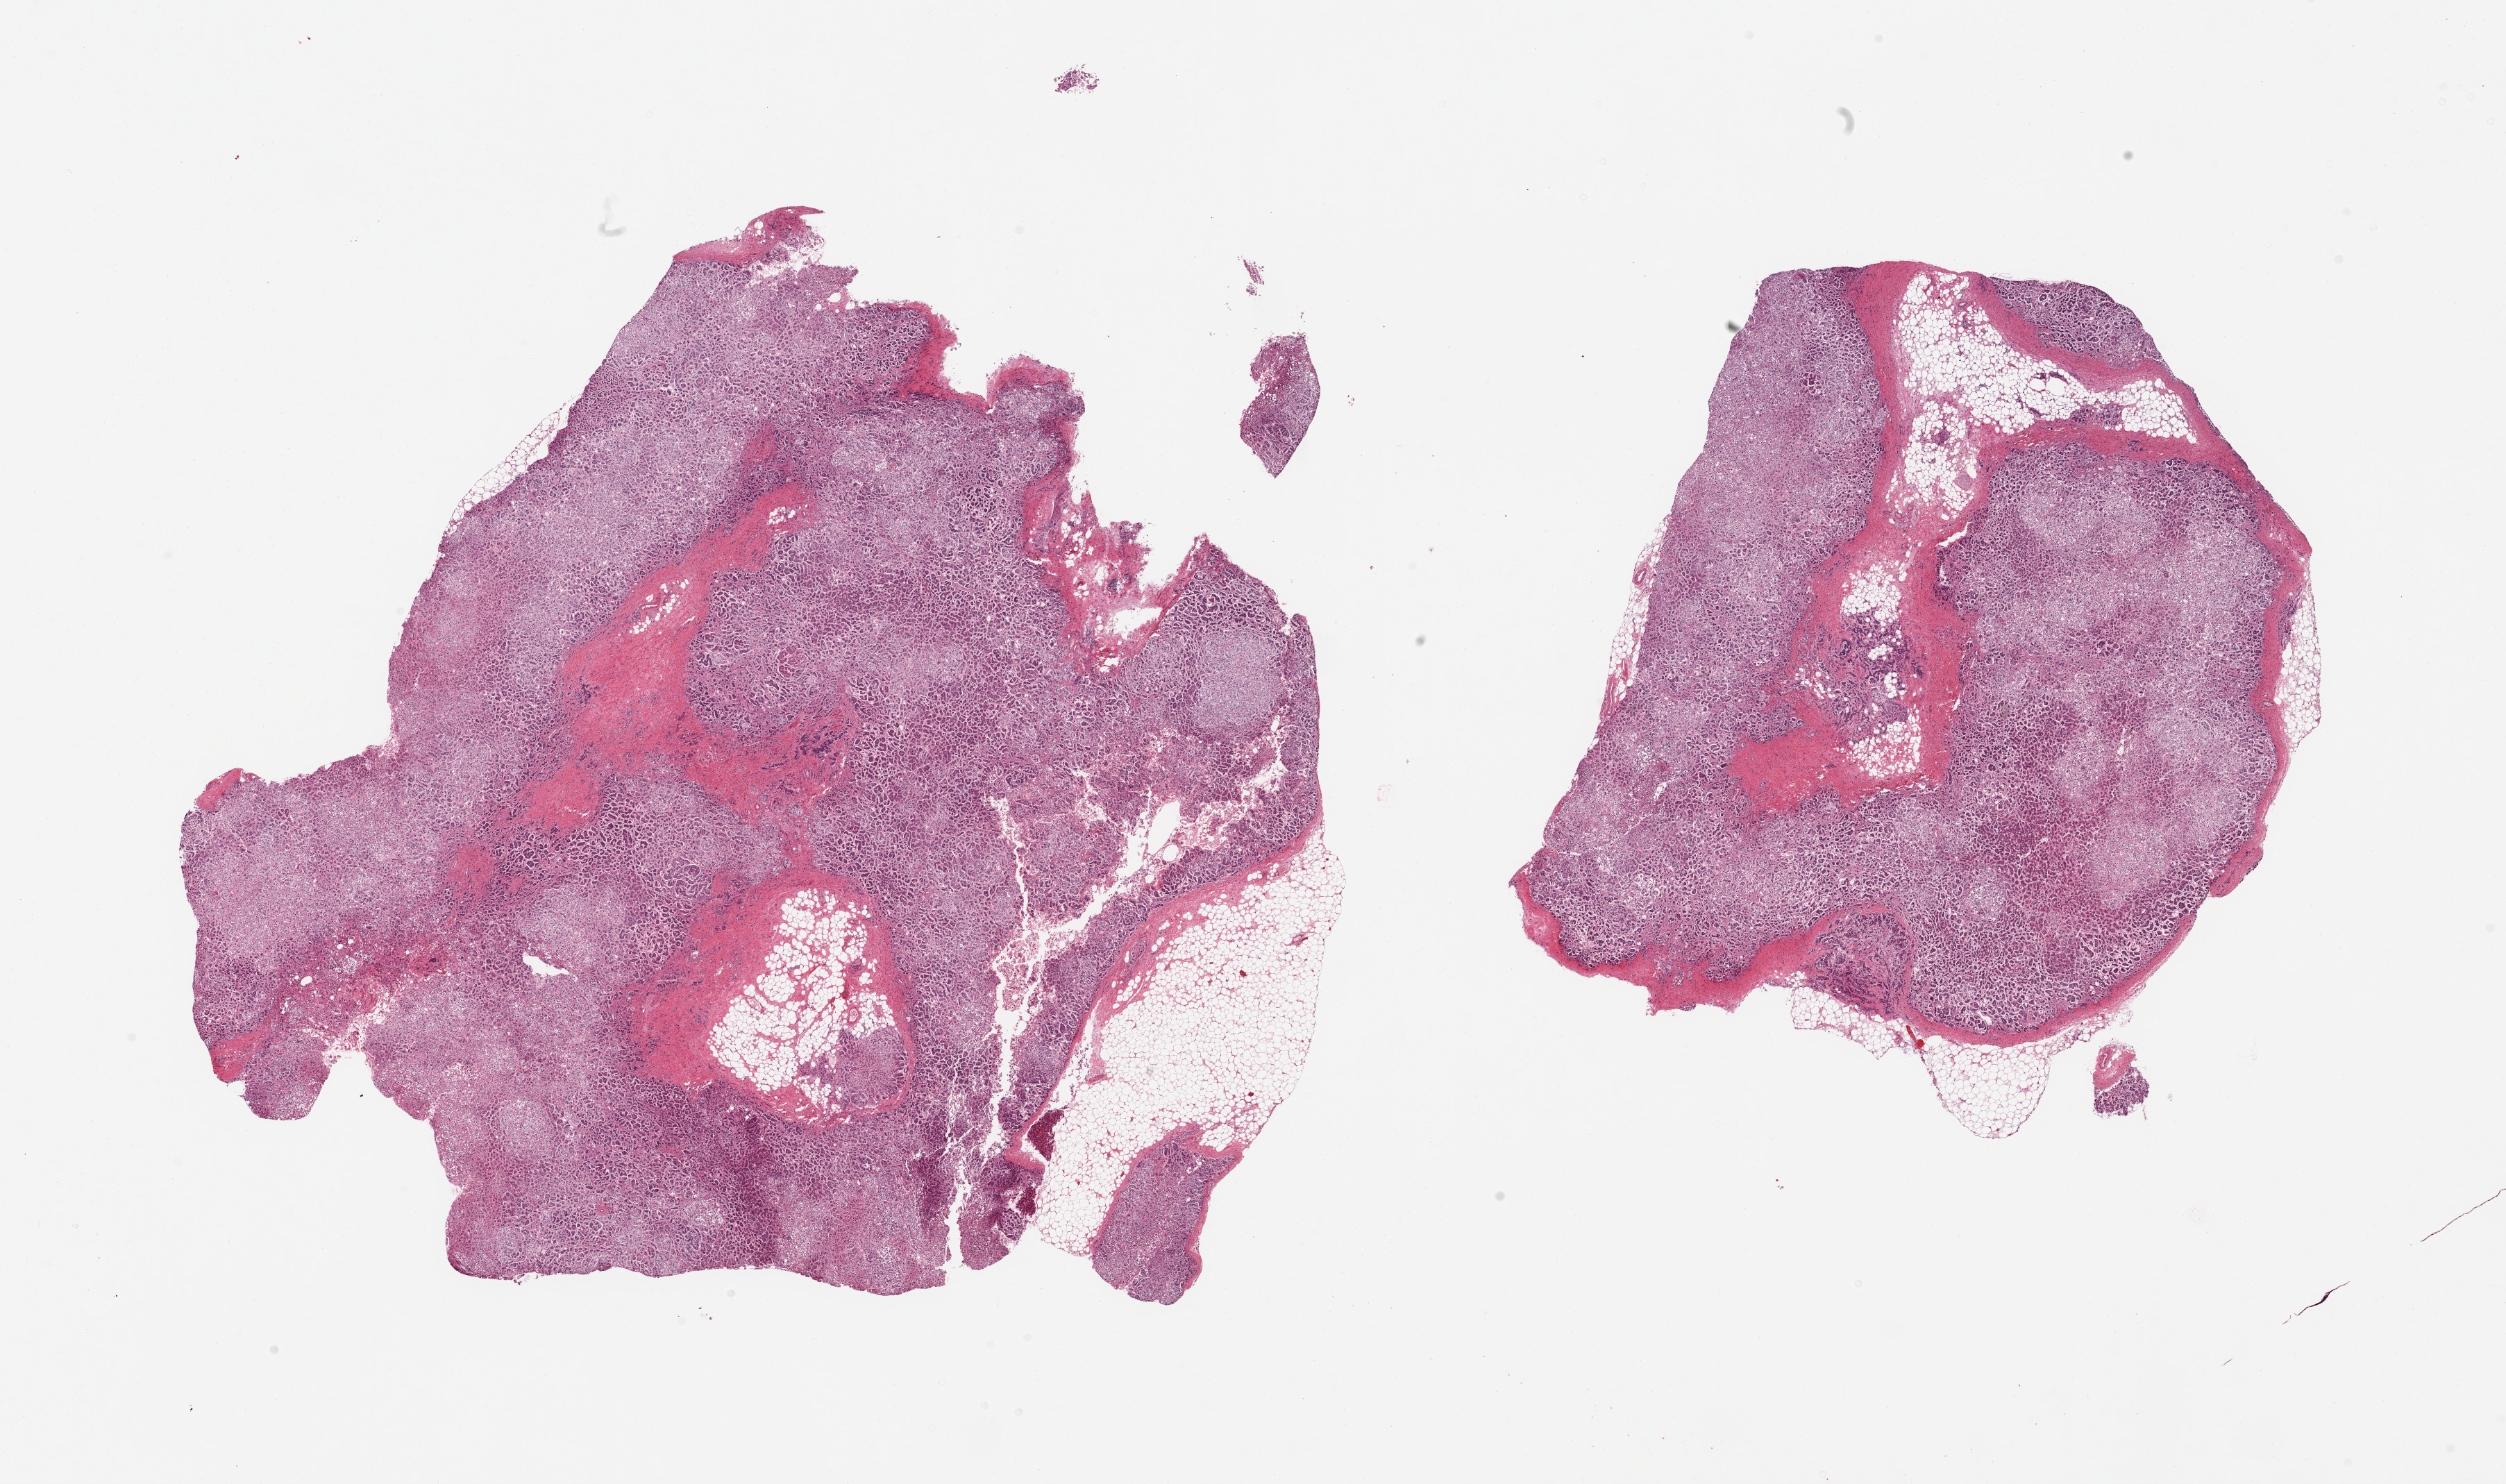
Digitized haematoxylin and eosin-stained section, brightfield, low-resolution overview of the scanned area, about 28.5 x 16.9 mm; PAXgene-fixed, paraffin-embedded tissue; target tissue: adrenal gland; tissue donor sample. Male donor.
- pathologist's review note for this sample: 2 pieces, ~20% adherent/interstitial fat; Trace adrenal meduall, fairly well preserved